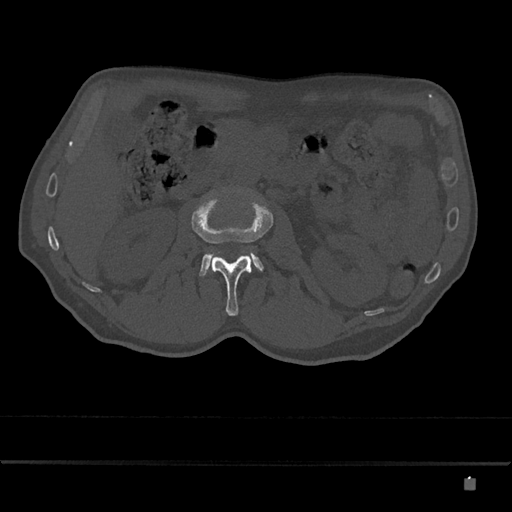
CT including the spine, one axial slice. Slice 457 of 797 in the series (ordered by position). Reconstruction kernel Br40s/3. 120 kVp. Bone window (W 1800 / L 400 HU). 0.5 mm slice thickness. 512 × 512 image matrix. Male patient, age 72 years. Case-level facts recorded for this patient, not image findings: primary cancer: prostate.
Structures marked on this image (semi-automatic segmentation, software-assisted and operator-edited):
- L2 vertebra: bounding box [x1, y1, x2, y2] px = [192, 196, 273, 316]
- L3 vertebra: [199, 252, 264, 276]